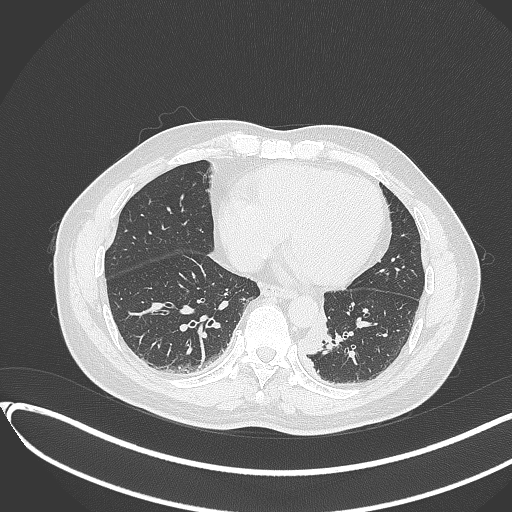
Chest CT, one axial slice; position 109 of 417 along the scan axis; reconstruction kernel B70f; lung window (W 1500 / L -600 HU); 1 mm slice thickness; 512 × 512 image matrix, field of view 400 × 400 mm. Male patient, age 54 years. Case-level facts recorded for this patient, not image findings: clinical TNM (as recorded): T3 N0 M0.
Outlined on this slice (rectangle marked by the reading radiologist):
- lung tumour (recorded histology: squamous cell carcinoma): bounding box [x1, y1, x2, y2] px = [302, 311, 331, 357]